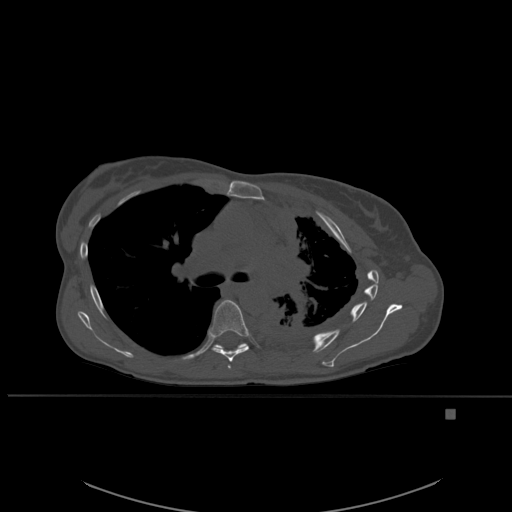
CT including the spine, one axial slice. Slice 380 of 537 in the series (ordered by position). Bone window (W 1800 / L 400 HU). 1.5 mm slice thickness. 512 × 512 image matrix, field of view 440 × 440 mm. Female patient, age 45 years. From the clinical record (not read from this slice): primary cancer: lung.
Annotated regions visible in this slice (semi-automatic segmentation, software-assisted and operator-edited):
- T5 vertebra: box from (x=228, y=364) to (x=231, y=369) px
- T6 vertebra: (x=209, y=300)–(x=249, y=362)
- T7 vertebra: (x=214, y=343)–(x=248, y=349)